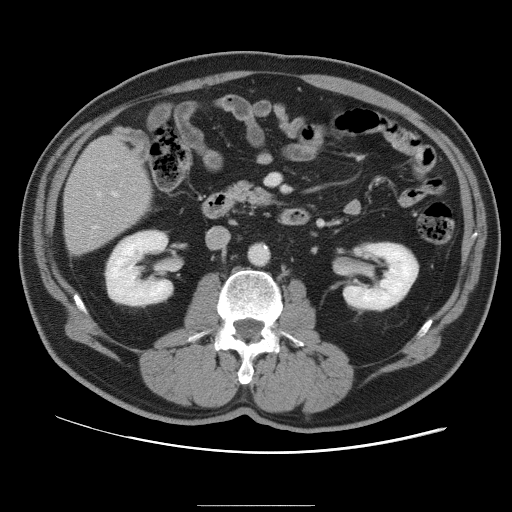
Contrast-enhanced abdominal CT, one axial slice. Position 34 of 105 along the scan axis. 120 kVp. Intravenous contrast given. Soft-tissue window (W 400 / L 40 HU). 5 mm slice thickness. 512 × 512 image matrix, field of view 399 × 399 mm. Male patient, age 64 years. From the clinical record (not read from this slice): diagnosis: colorectal cancer liver metastases, imaged before liver resection; multiple liver metastases: yes.
Annotated regions visible in this slice (expert manual segmentation):
- hepatic veins: box from (x=93, y=192) to (x=118, y=228) px
- liver: (x=64, y=138)–(x=150, y=253)
- planned liver remnant (the part of the liver to remain after resection): (x=64, y=138)–(x=150, y=236)
- portal vein (with intrahepatic branches): (x=97, y=192)–(x=101, y=197)